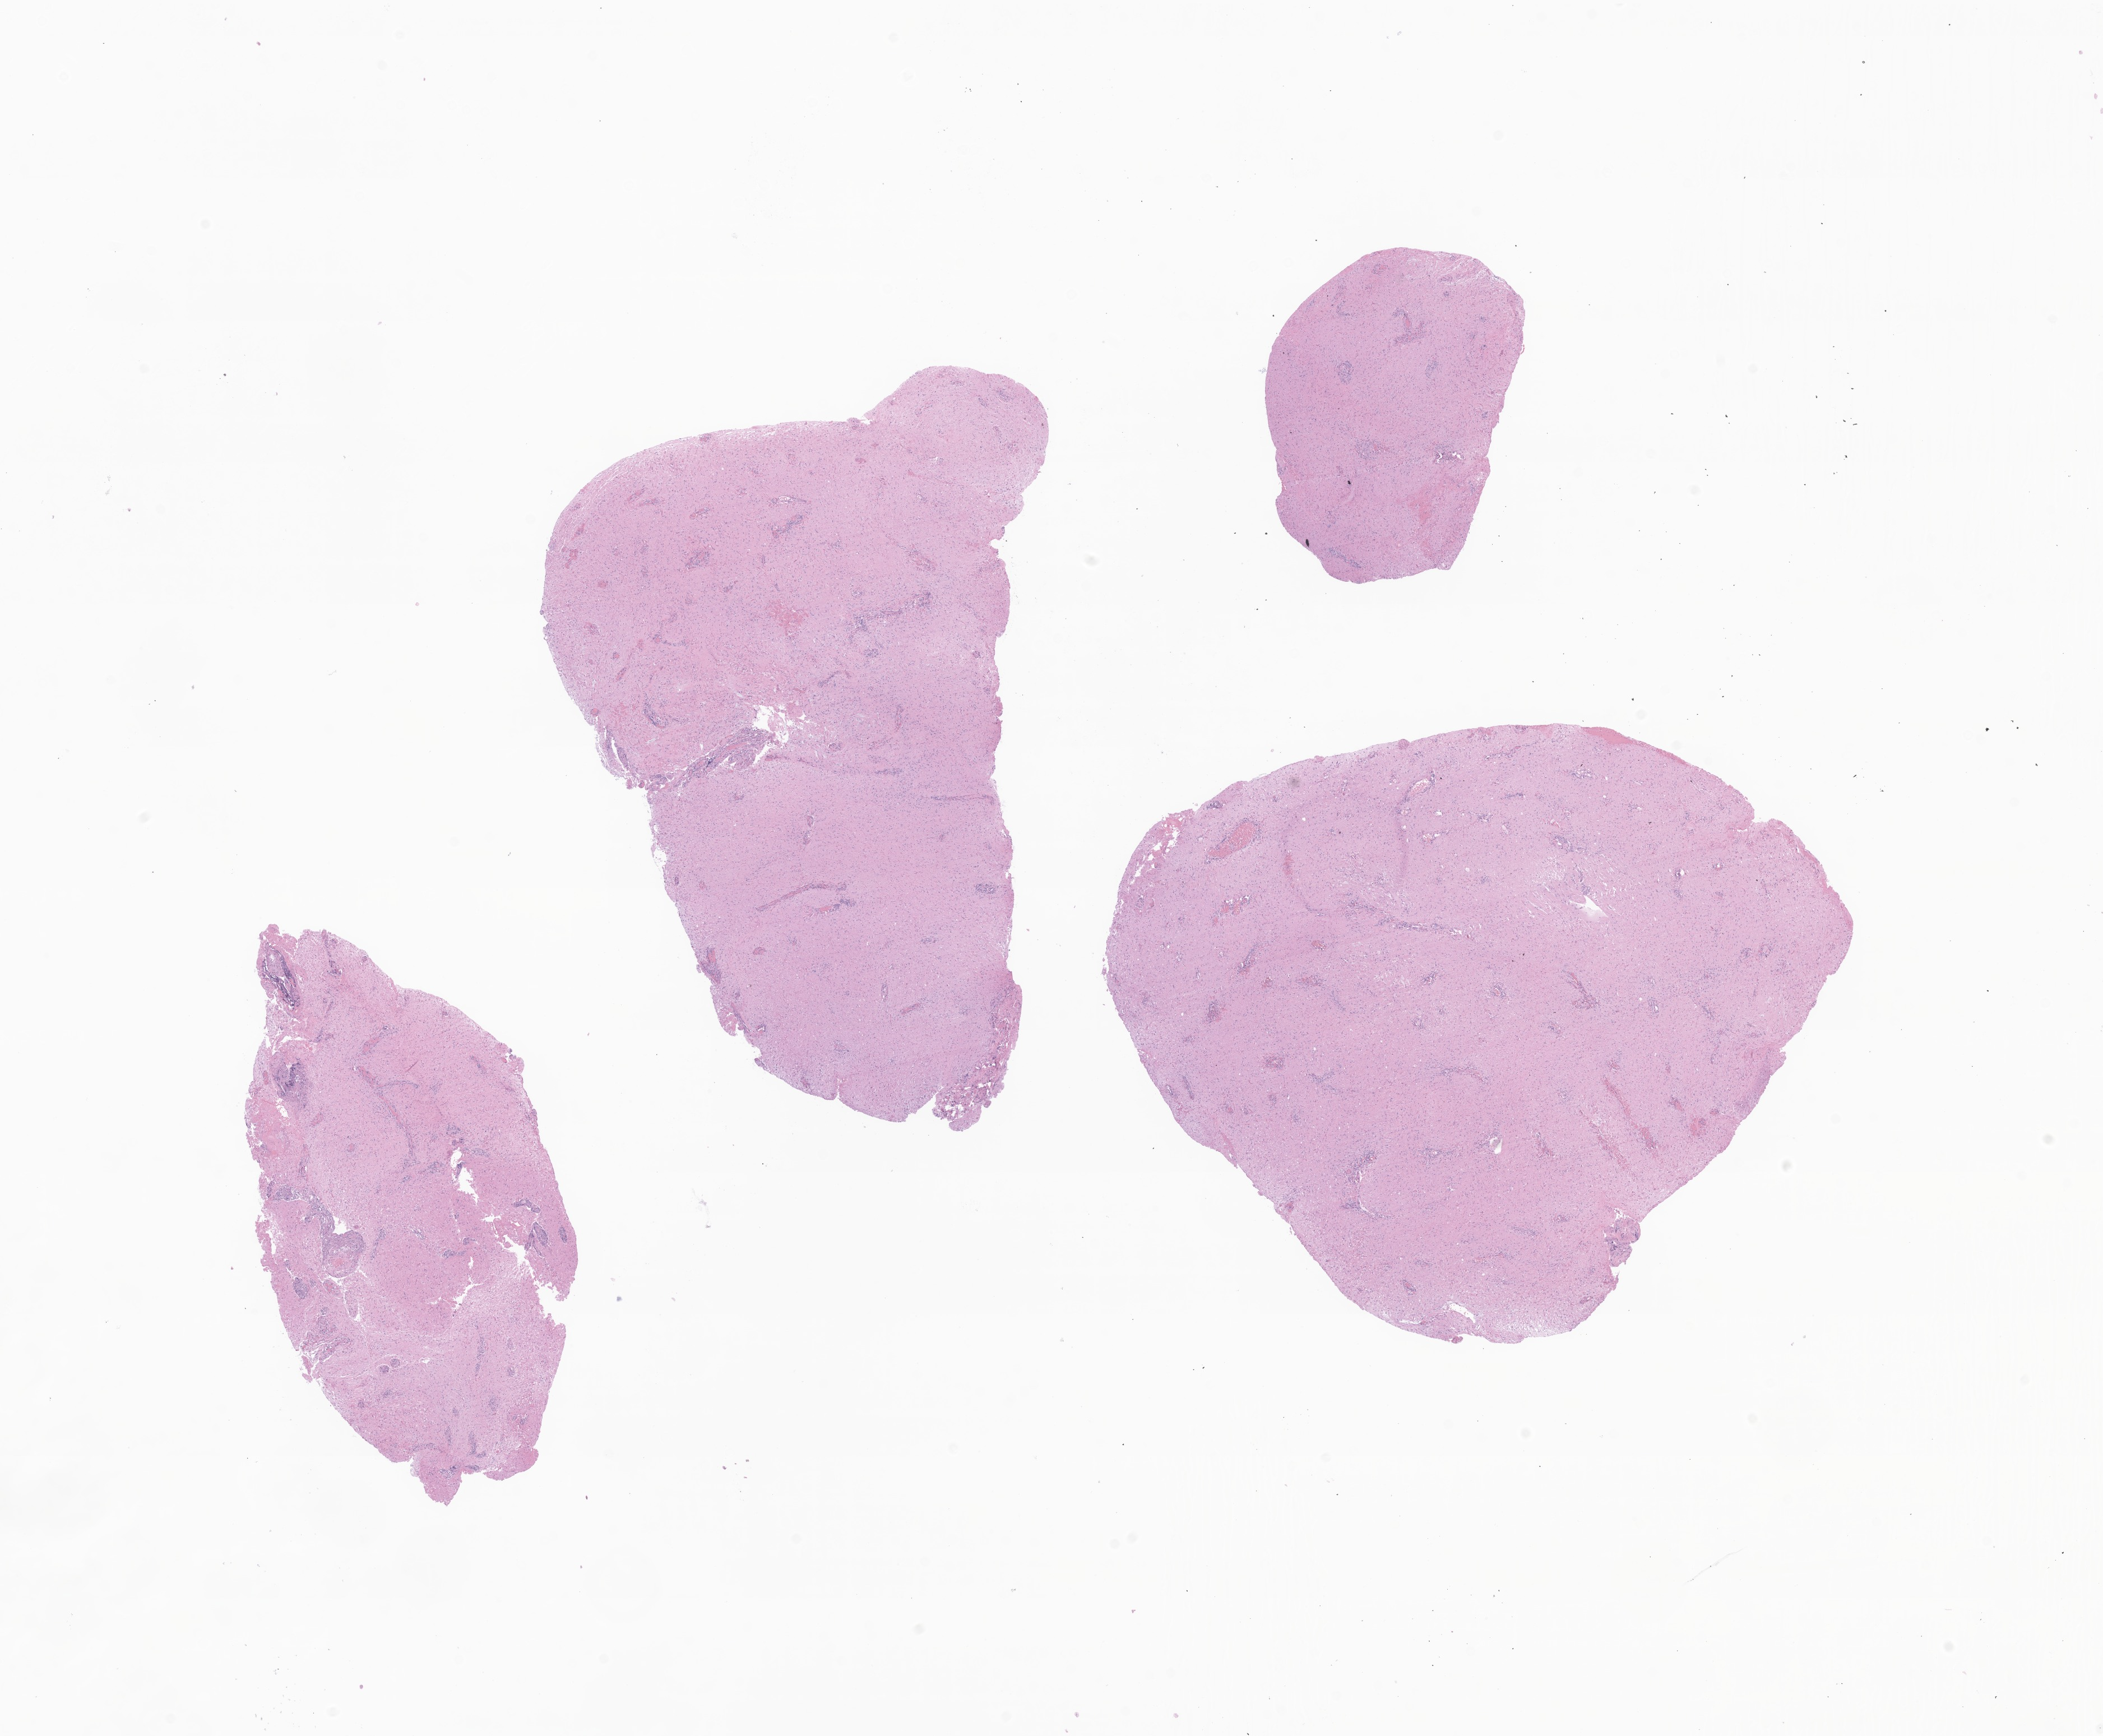
Whole-slide image, H&E stain of tumor tissue from the brain, a low-resolution overview of the entire scanned area, about 15.8 x 13.1 mm, FFPE section. Patient: female, age 208 months (17 years 4 months).
Diagnosis: Neoplasm, uncertain whether benign or malignant.